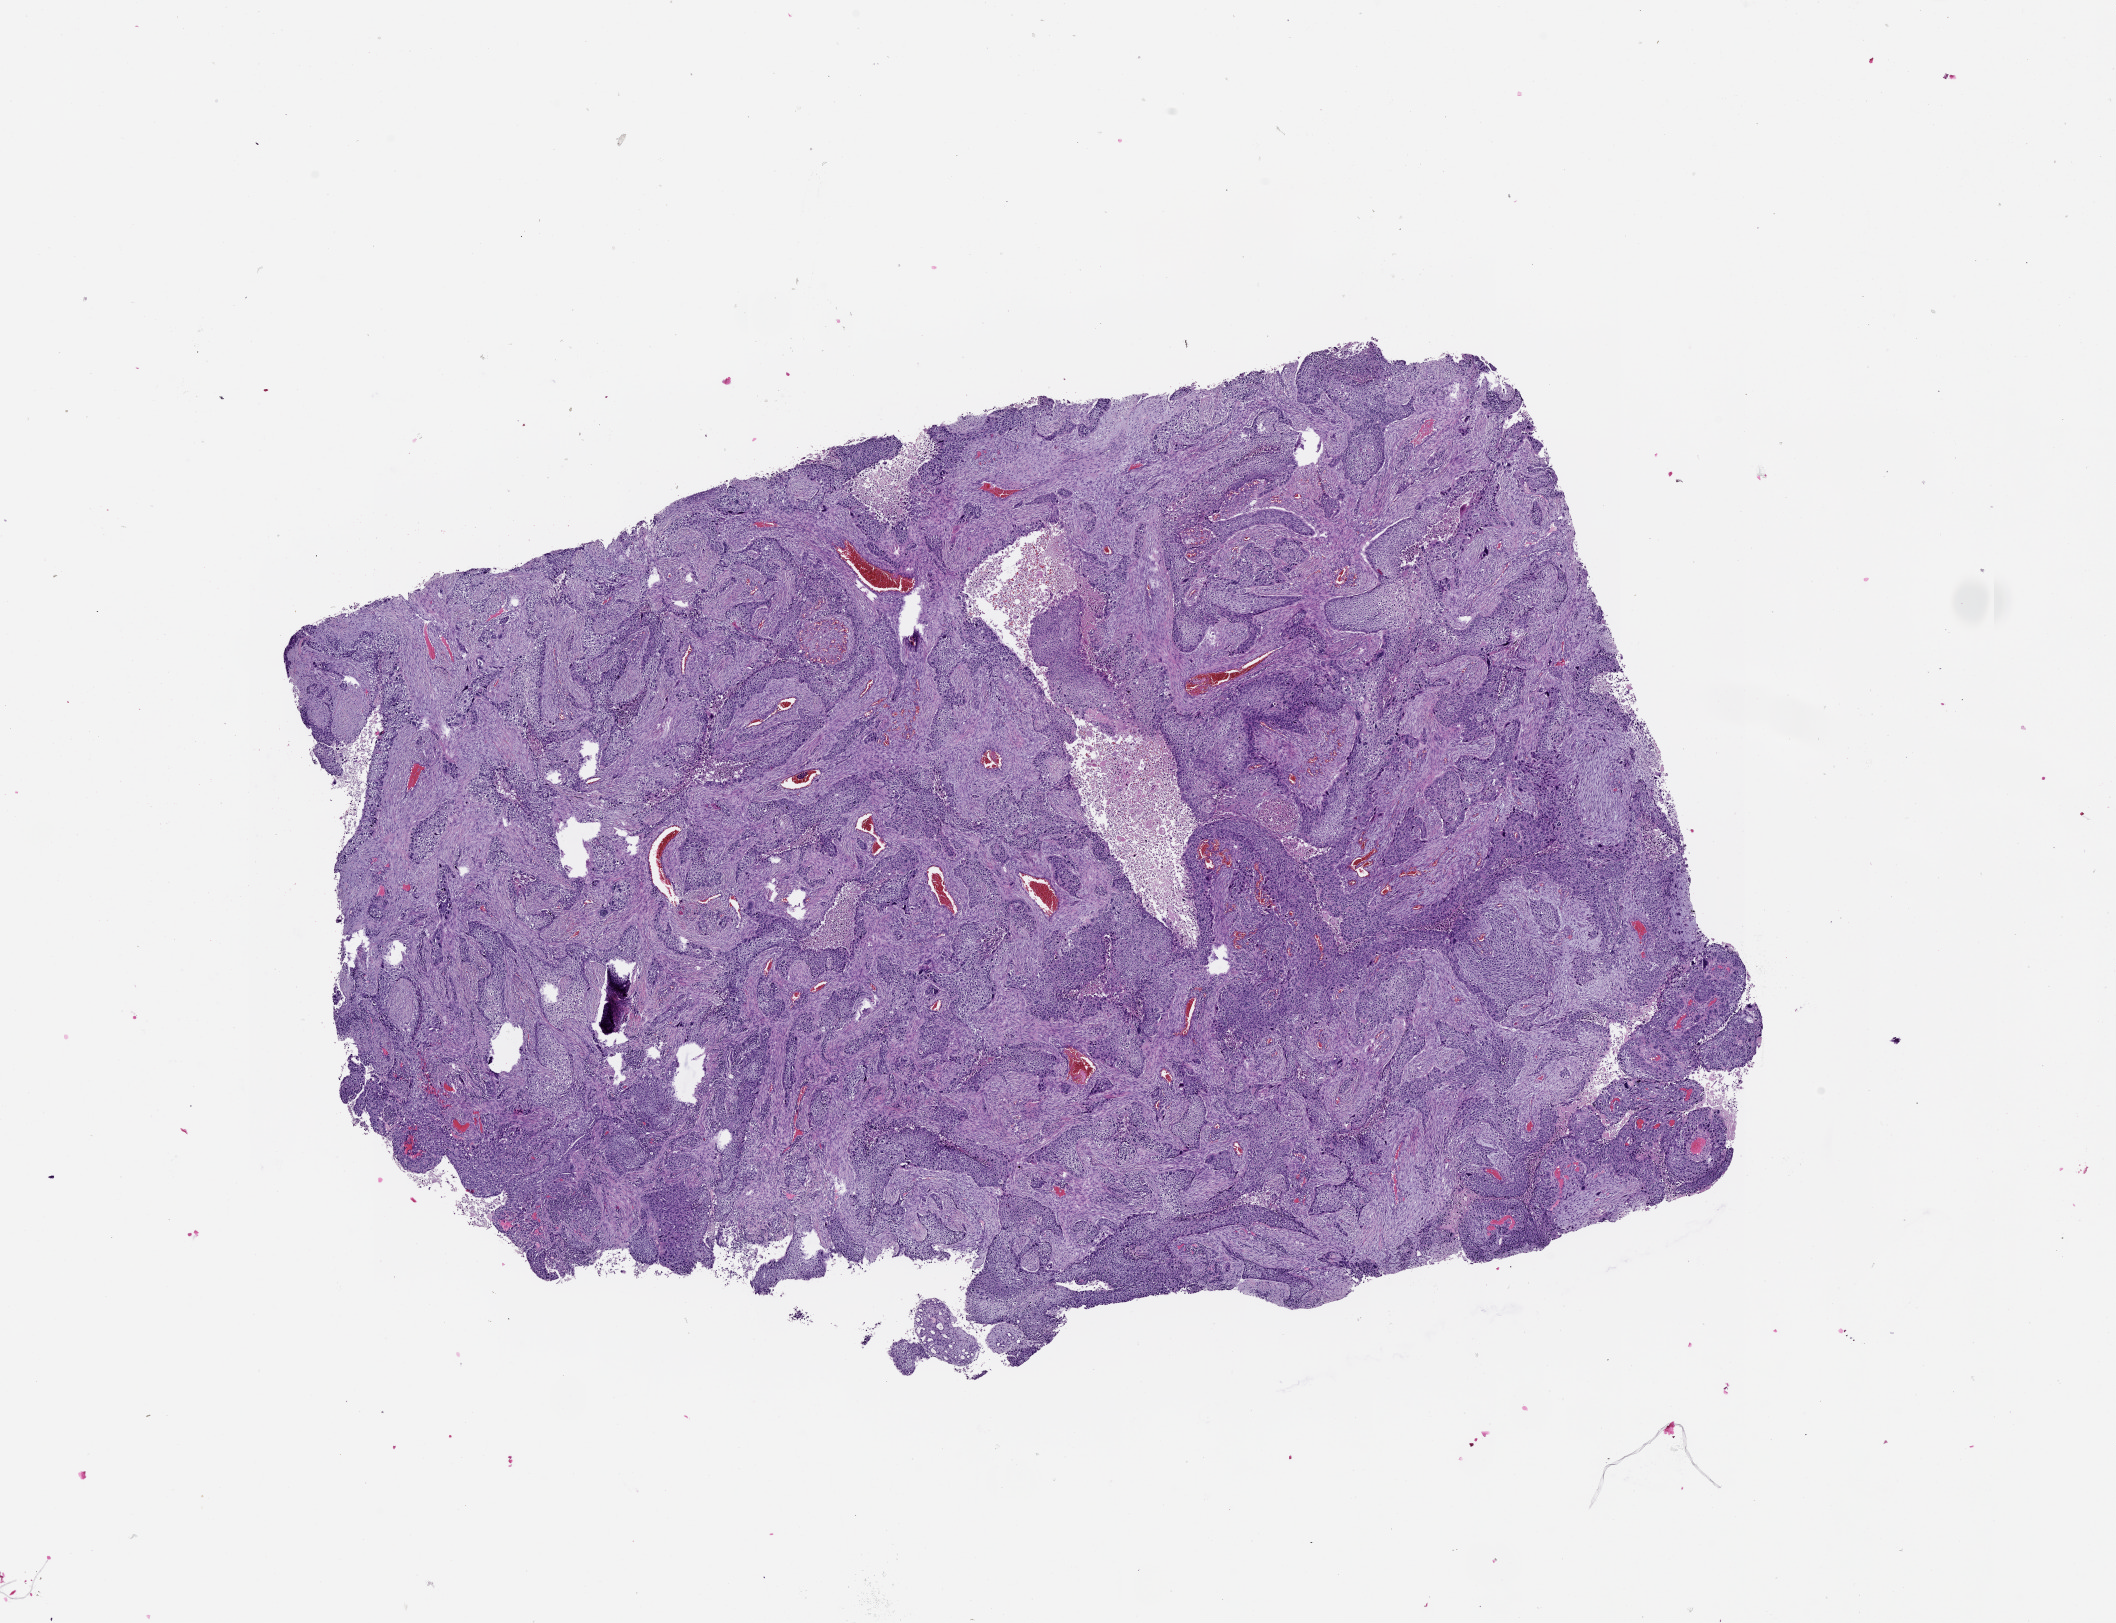
Digitized H&E-stained tissue section (whole slide) — low-resolution overview of the scanned area, about 17.0 x 13.1 mm (from a 20x scan). Tumour tissue sample, lung. Male, 55 y/o.
Patient diagnosis (cohort enrolment): squamous cell carcinoma (lung).